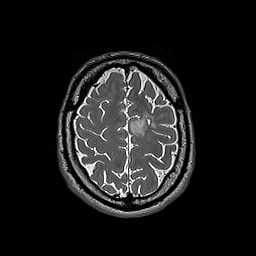
Brain MRI from a brain-tumour surgery series, one axial slice. 1 mm slice thickness. 256 × 256 image matrix. From the clinical record (not read from this slice): histopathology: Oligodendroglioma; WHO grade: 3; IDH mutation: yes.
Structures marked on this image (outlined manually by an expert reader):
- tumour: bounding box <131,114,156,136> (left, top, right, bottom; pixels)